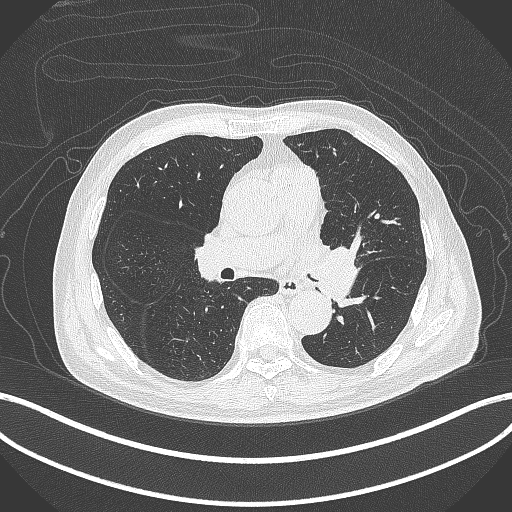
Chest CT, one axial slice. Position 234 of 417 along the scan axis. Lung window (W 1500 / L -600 HU). 1 mm slice thickness. 512 × 512 image matrix, field of view 400 × 400 mm. Male patient, age 77 years. From the clinical record (not read from this slice): clinical TNM (as recorded): T3 N1 M0.
Structures marked on this image (rectangle marked by the reading radiologist):
- lung tumour (recorded histology: adenocarcinoma): bounding box (x1, y1, x2, y2) in pixels: (310, 231, 363, 301)